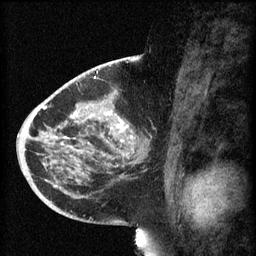
Breast MRI (dynamic contrast-enhanced), one sagittal slice; slice 32 of 60 in the series (ordered by position); 3 images stored at this slice position (order not interpretable as contrast timing); 1.5 T; TE 4.2 ms, TR 8.1 ms; 2 mm slice thickness; 256 × 256 image matrix. Female patient, age 44 years.
Outlined on this slice (semi-automatic segmentation, software-assisted and operator-edited):
- analysis volume of interest (the breast-tissue region the enhancement analysis was run in; not a lesion): bounding box (x1, y1, x2, y2) in pixels: (59, 110, 151, 169)
- tumour enhancement mask (voxels above the 70 % enhancement threshold inside the analysis volume of interest): (61, 112, 133, 157)